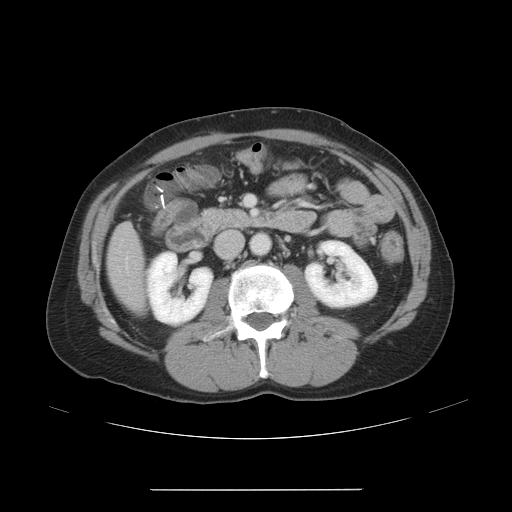
Contrast-enhanced abdominal CT, one axial slice. Reconstruction kernel STANDARD. 120 kVp. Intravenous contrast given. Soft-tissue window (W 400 / L 40 HU). 5 mm slice thickness. 512 × 512 image matrix, field of view 409 × 409 mm. Male patient, age 56 years. From the clinical record (not read from this slice): diagnosis: colorectal cancer liver metastases, imaged before liver resection; multiple liver metastases: yes; largest metastasis: 1.8 cm; chemotherapy before resection: yes.
Annotated regions visible in this slice (manually delineated by an expert):
- hepatic veins: bounding box <125,256,129,270> (left, top, right, bottom; pixels)
- liver: <109,225,145,311>
- planned liver remnant (the part of the liver to remain after resection): <111,271,145,311>